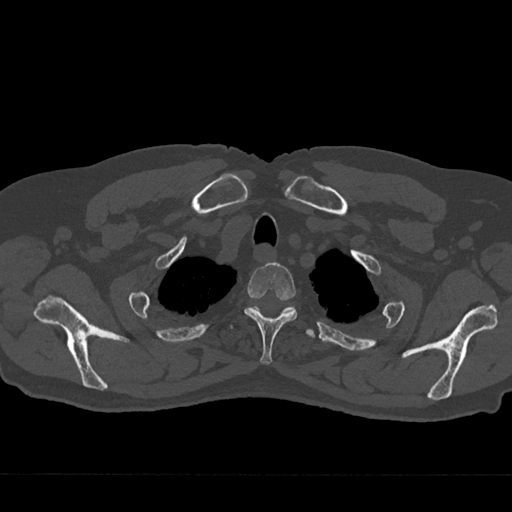
CT including the spine, one axial slice; position 604 of 797 along the scan axis; 120 kVp; bone window (W 1800 / L 400 HU); 0.5 mm slice thickness; 512 × 512 image matrix, field of view 377 × 377 mm. Patient: male, 75 years. Case-level facts recorded for this patient, not image findings: primary cancer: renal; vertebrae with lytic lesions (as recorded): T4.
Outlined on this slice (semi-automatically segmented with operator editing):
- T2 vertebra: box from (x=244, y=262) to (x=297, y=365) px
- T3 vertebra: (x=230, y=306)–(x=315, y=338)